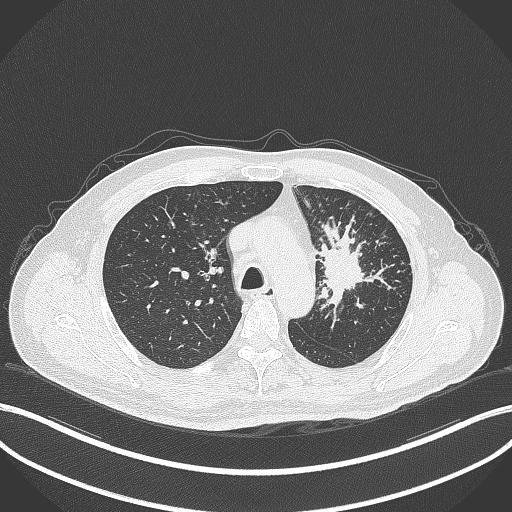
Chest CT, one axial slice. Lung window (W 1500 / L -600 HU). 512 × 512 image matrix, field of view 400 × 400 mm. Patient: male, 69 years. Case-level facts recorded for this patient, not image findings: clinical TNM (as recorded): T2a N2 M0; histopathological grade: G2-3.
Outlined on this slice (rectangle marked by the reading radiologist):
- lung tumour (recorded histology: adenocarcinoma): bounding box (x1, y1, x2, y2) in pixels: (308, 223, 372, 311)